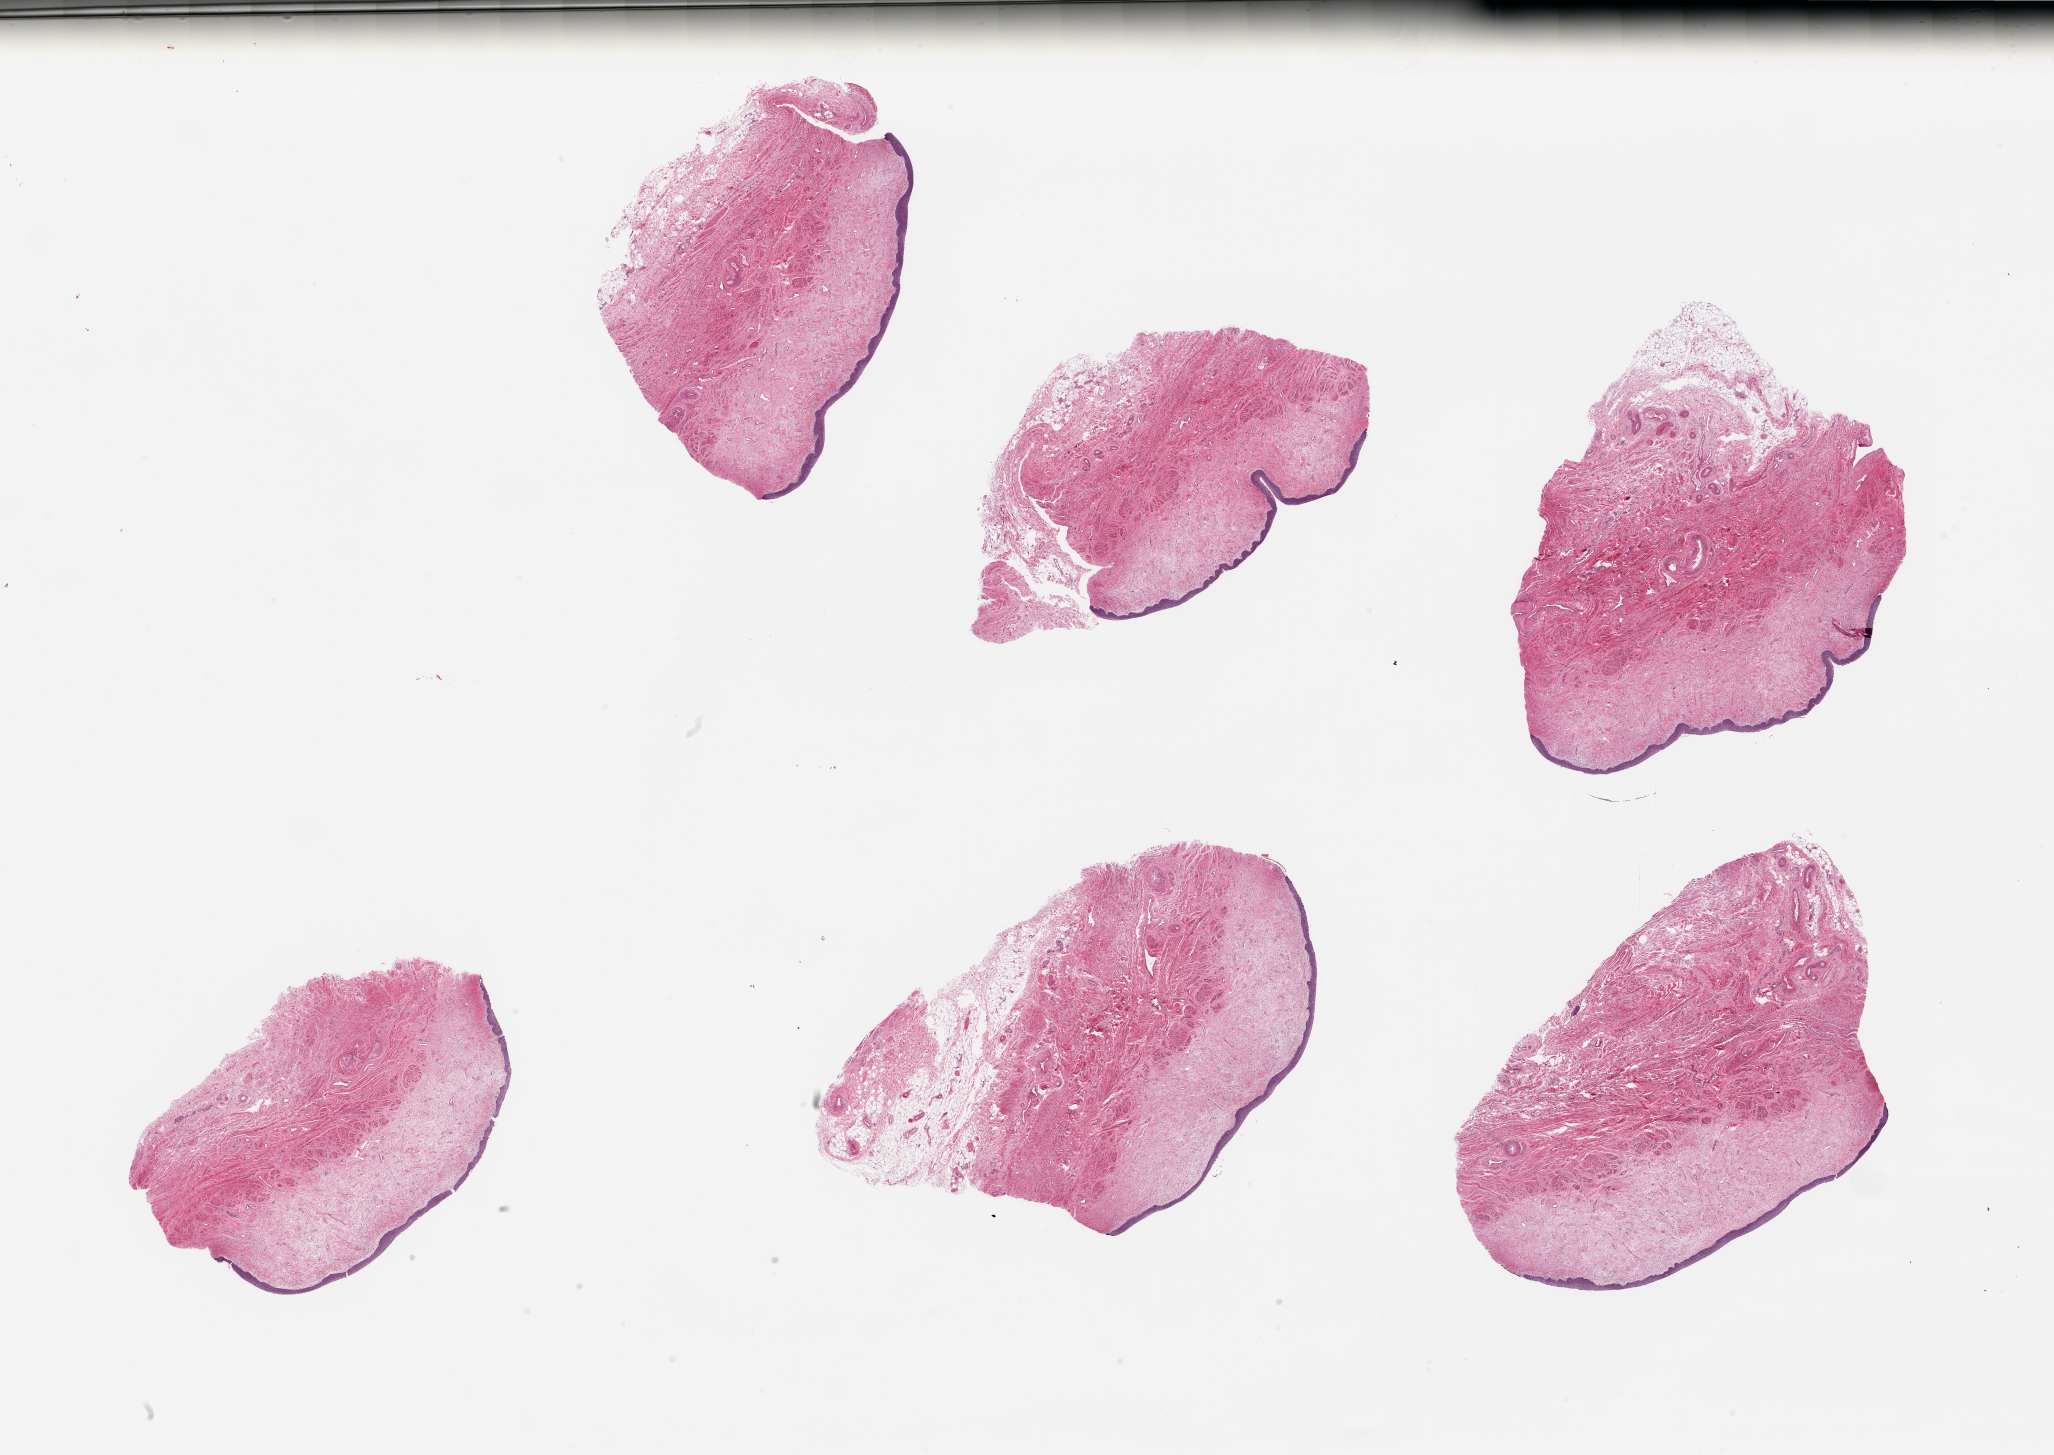
Whole-slide image, hematoxylin and eosin (H&E) stain, a low-resolution overview of the entire scanned area, about 32.5 x 23.0 mm (from a 20x scan). PAXgene-fixed paraffin-embedded (PFPE) section. Target tissue: vagina. Tissue donor sample. Female donor.
Pathologist's review note for this sample: 6 pieces; well preserved epithelium.